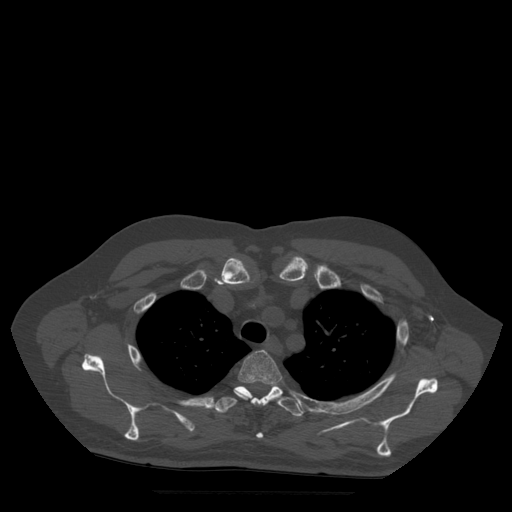
CT including the spine, one axial slice; position 401 of 522 along the scan axis; bone window (W 1800 / L 400 HU); 1.25 mm slice thickness; 512 × 512 image matrix, field of view 420 × 420 mm. Patient age 72 years. From the clinical record (not read from this slice): primary cancer: prostate.
Outlined on this slice (semi-automatic segmentation, software-assisted and operator-edited):
- T3 vertebra: bounding box (x1, y1, x2, y2) in pixels: (239, 350, 283, 439)
- T4 vertebra: (214, 384, 305, 417)